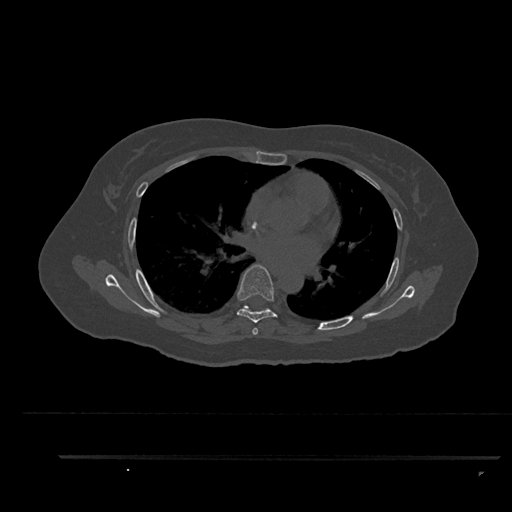
CT including the spine, one axial slice. Position 555 of 797 along the scan axis. 120 kVp. Bone window (W 1800 / L 400 HU). 0.5 mm slice thickness. 512 × 512 image matrix, field of view 408 × 408 mm. Female patient, age 44 years. Case-level facts recorded for this patient, not image findings: primary cancer: renal; vertebrae with lytic lesions (as recorded): L1.
Structures marked on this image (semi-automatically segmented with operator editing):
- T5 vertebra: bounding box (x1, y1, x2, y2) in pixels: (254, 328, 257, 334)
- T6 vertebra: (236, 264, 278, 335)